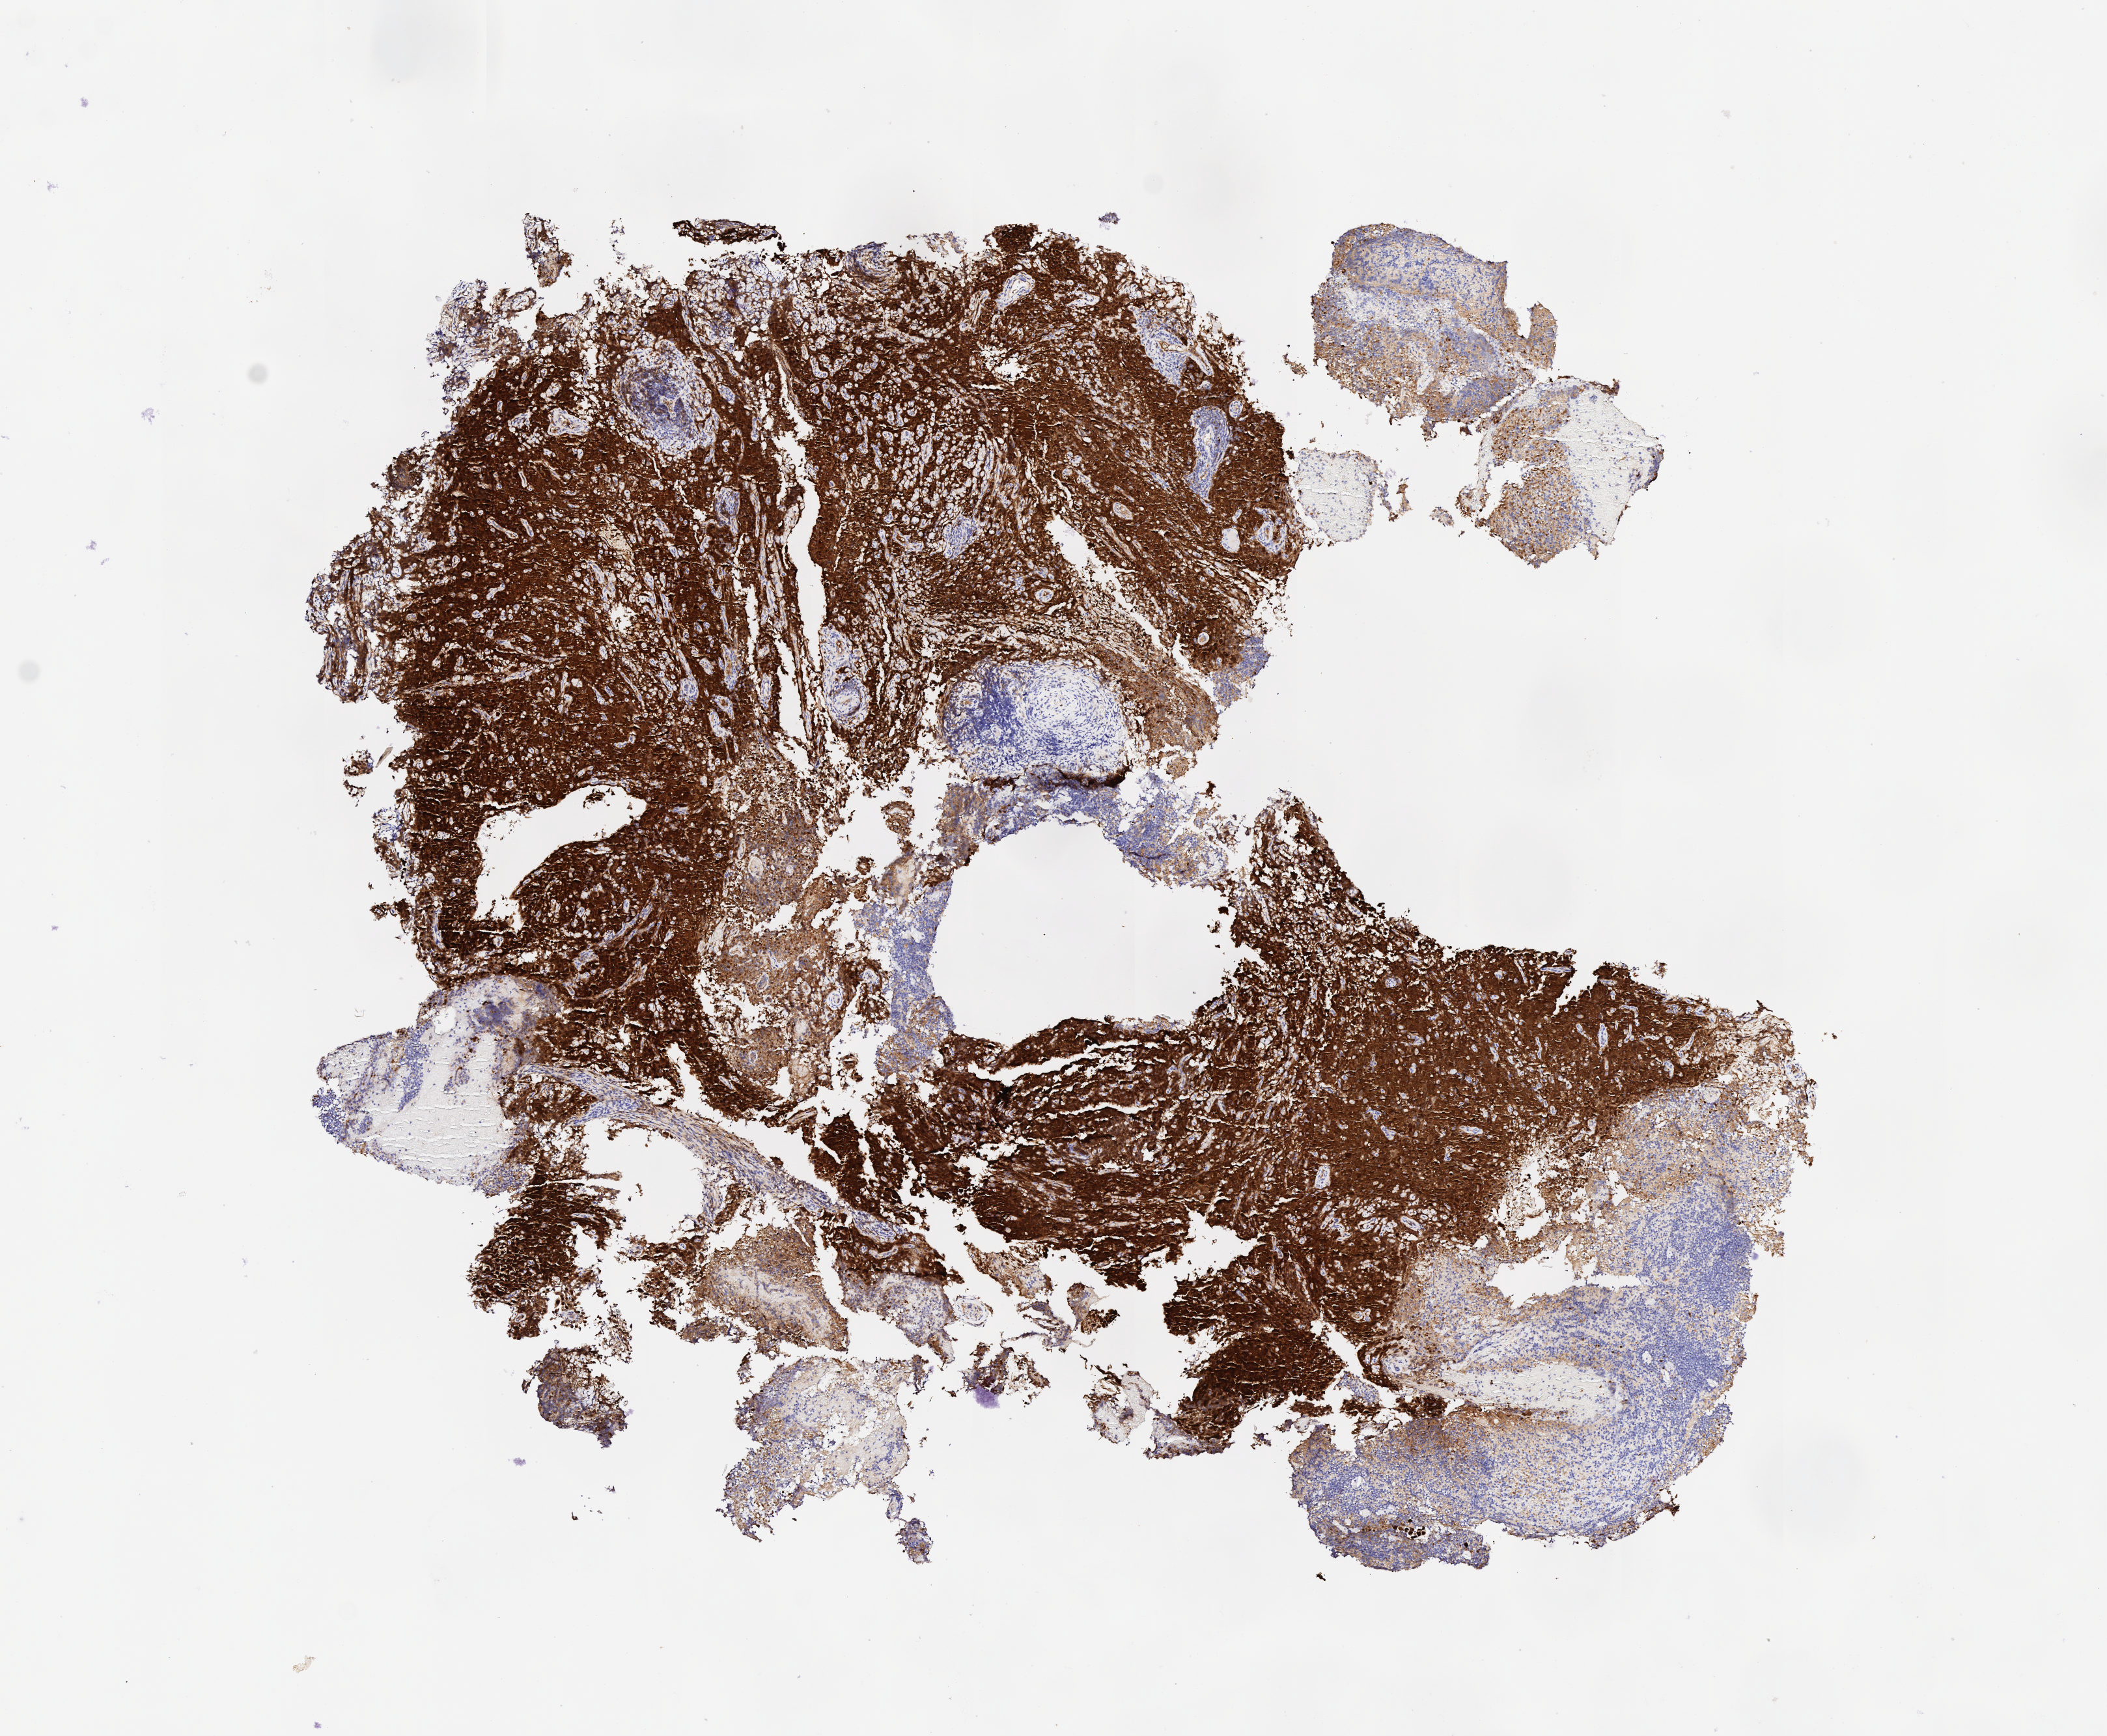
IHC for p16 (p16INK4a), whole-slide image, shown as a low-resolution overview of the whole scanned area (about 6.5 x 5.4 mm). Specimen: tumor tissue. Site: cervix. Female patient, age 42 years.
* diagnosis: Squamous cell carcinoma, large cell, nonkeratinizing, NOS